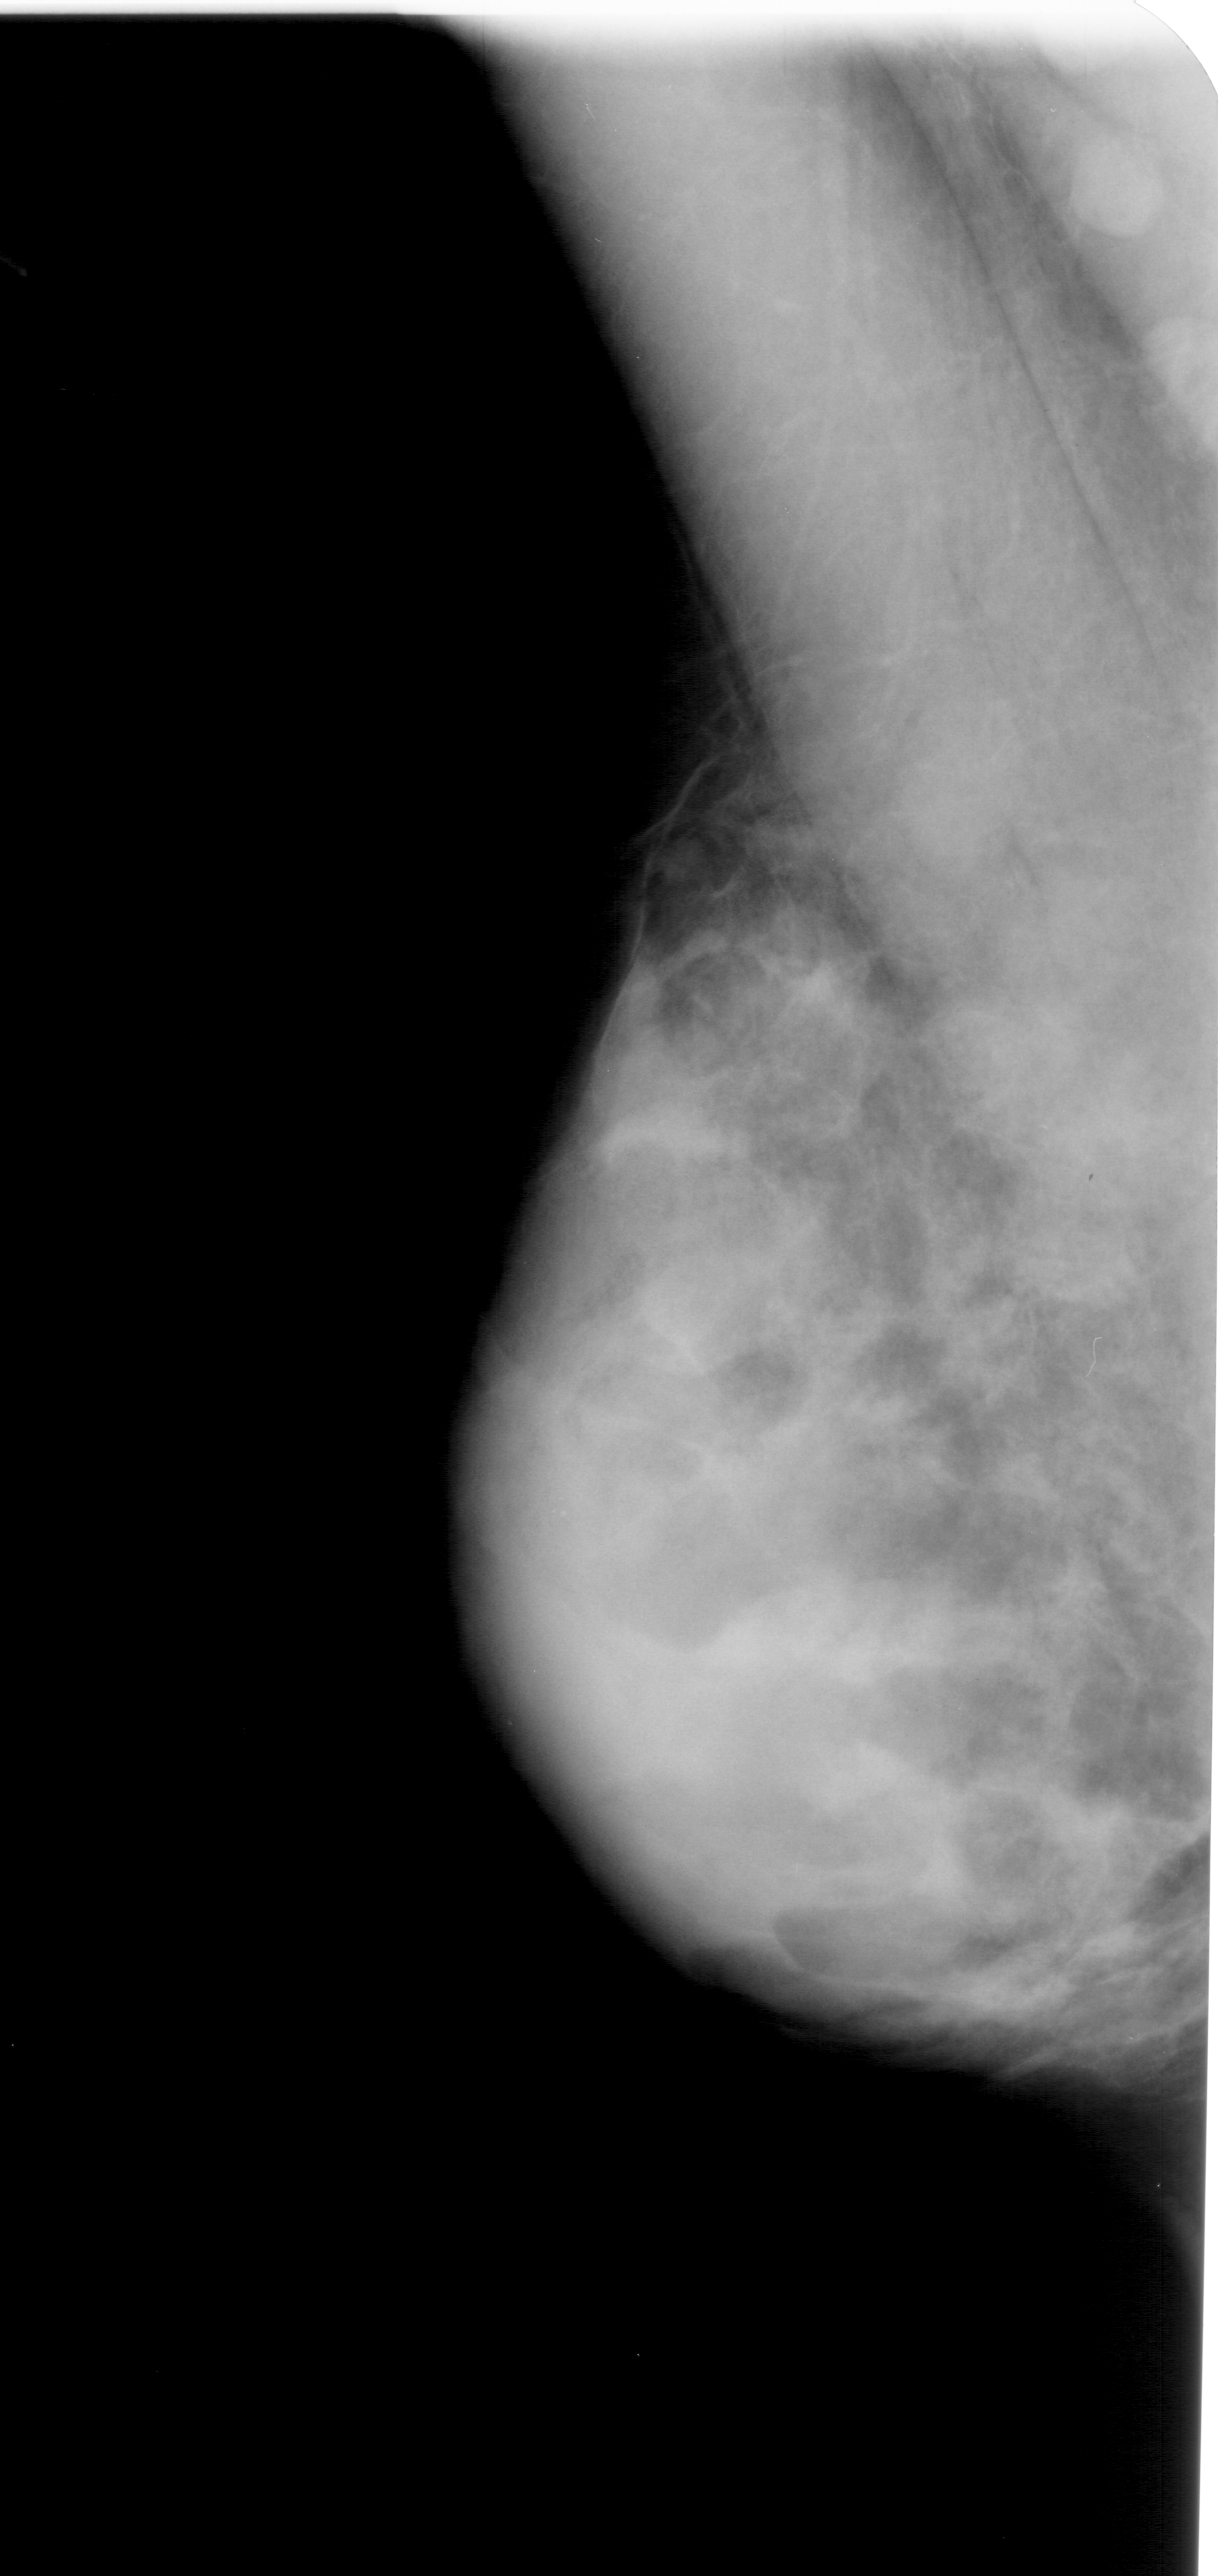
Scanned film-screen mammogram; left breast; mediolateral oblique (MLO) view; BI-RADS breast density category 4 (scale 1–4); 1218 × 2576 image matrix.
Expert-marked regions of interest on this film, with their recorded descriptors:
- calcifications, morphology pleomorphic, distribution clustered; BI-RADS assessment category 4; subtlety rating 1 on a 1 (subtle) to 5 (obvious) scale; pathology (as recorded): benign: bounding box <538,1483,581,1534> (left, top, right, bottom; pixels)